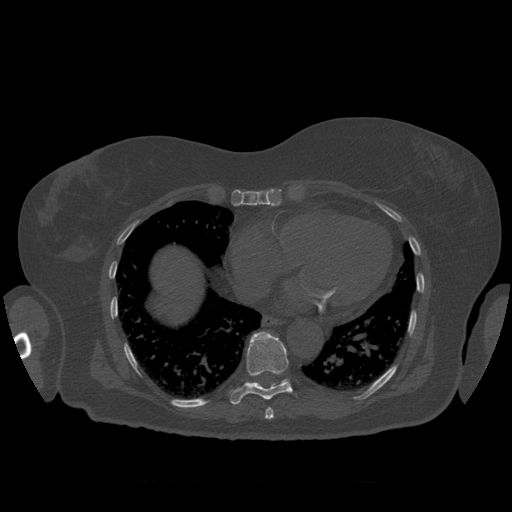
CT including the spine, one axial slice; slice 358 of 399 in the series (ordered by position); 120 kVp; bone window (W 1800 / L 400 HU); 512 × 512 image matrix. Patient age 81 years. From the clinical record (not read from this slice): primary cancer: renal; vertebrae with lytic lesions (as recorded): L1.
Outlined on this slice (semi-automatically segmented with operator editing):
- T10 vertebra: bounding box (x1, y1, x2, y2) in pixels: (276, 379, 291, 386)
- T8 vertebra: (265, 408, 274, 420)
- T9 vertebra: (230, 332, 293, 405)